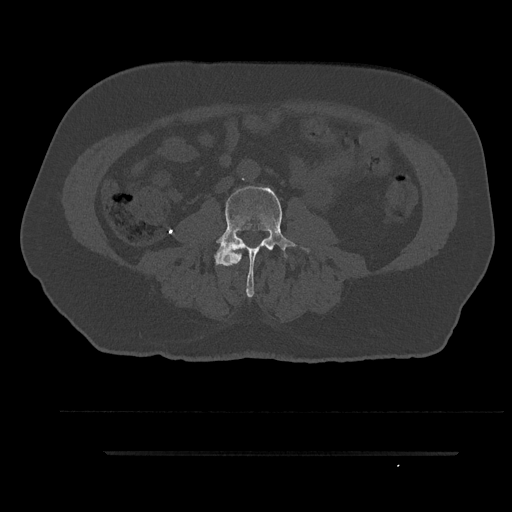
CT including the spine, one axial slice. Position 40 of 797 along the scan axis. Reconstruction kernel Br40s/3. 120 kVp. Bone window (W 1800 / L 400 HU). 512 × 512 image matrix, field of view 432 × 432 mm. Male patient, age 63 years. Case-level facts recorded for this patient, not image findings: primary cancer: renal; vertebrae with lytic lesions (as recorded): T8.
Structures marked on this image (semi-automatic segmentation, software-assisted and operator-edited):
- L2 vertebra: bounding box (x1, y1, x2, y2) in pixels: (238, 255, 242, 260)
- L3 vertebra: (202, 185, 310, 298)